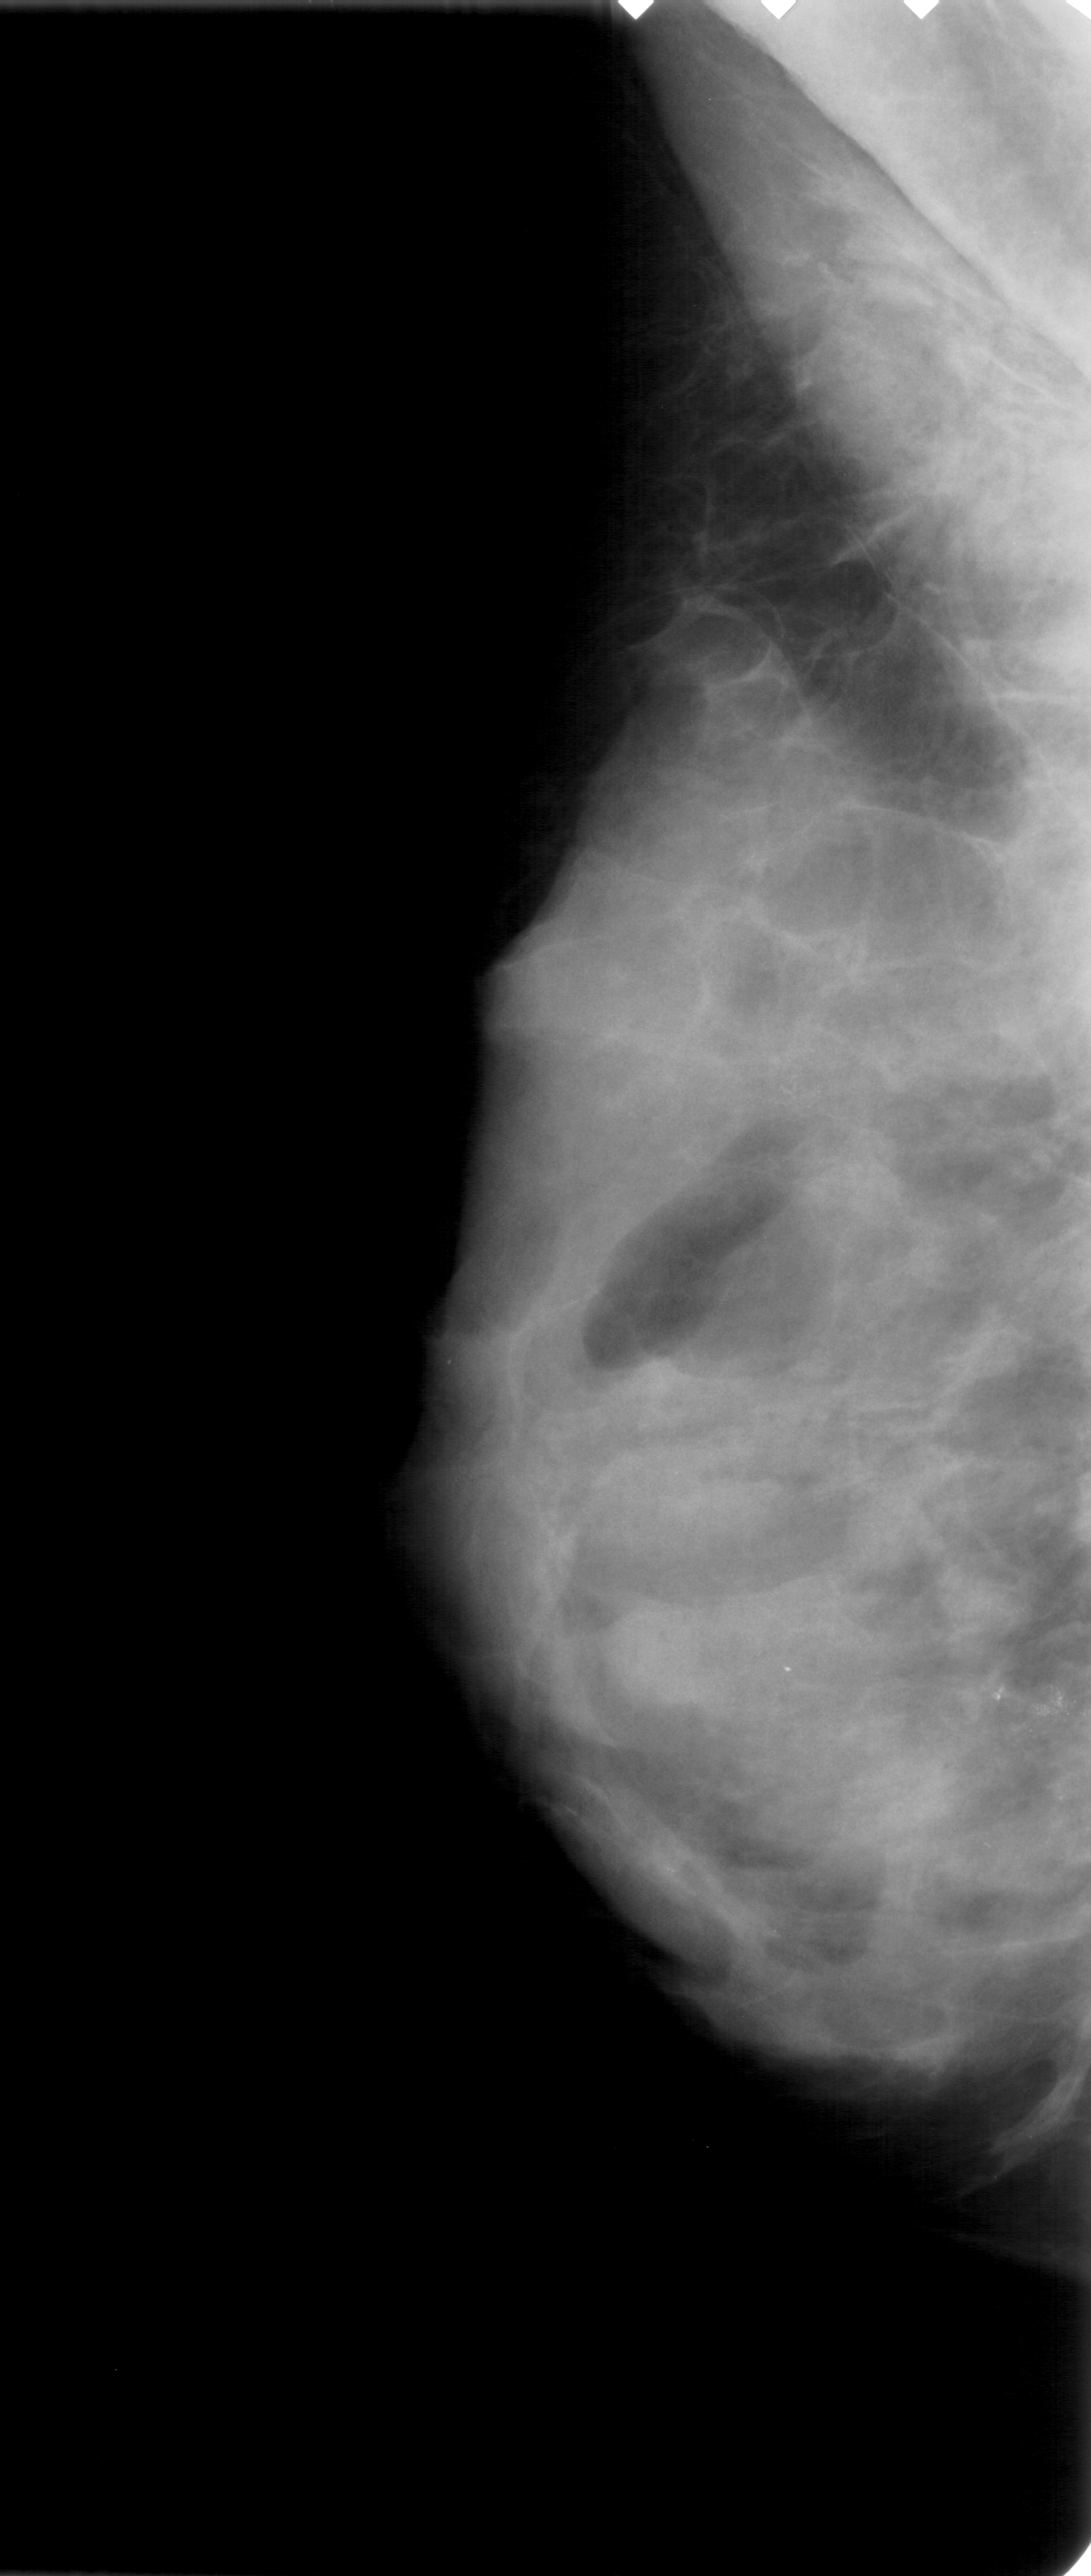
Scanned film-screen mammogram, left breast, MLO view.
Radiologist-marked abnormalities on this image: Finding 1 of 2: calcifications, morphology pleomorphic, distribution clustered; BI-RADS assessment category 4; subtlety rating 3 on a 1 (subtle) to 5 (obvious) scale; pathology (as recorded): malignant. Finding 2 of 2: calcifications, morphology pleomorphic, distribution clustered; BI-RADS assessment category 4; pathology (as recorded): malignant.